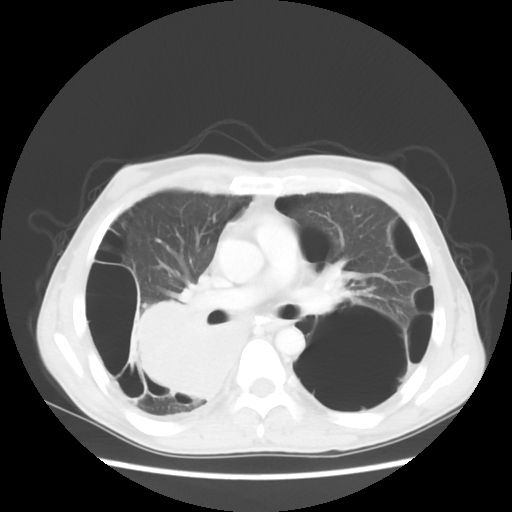
Chest CT, one axial slice. Position 31 of 56 along the scan axis. Reconstruction kernel STANDARD. 140 kVp. Lung window (W 1500 / L -600 HU). 512 × 512 image matrix, field of view 351 × 351 mm. Patient: male, 41 years. Case-level facts recorded for this patient, not image findings: clinical TNM (as recorded): T4 N0 M1a; histopathological grade: G3.
Outlined on this slice (bounding box drawn by a radiologist):
- lung tumour (recorded histology: large cell carcinoma): box from (x=124, y=299) to (x=242, y=413) px